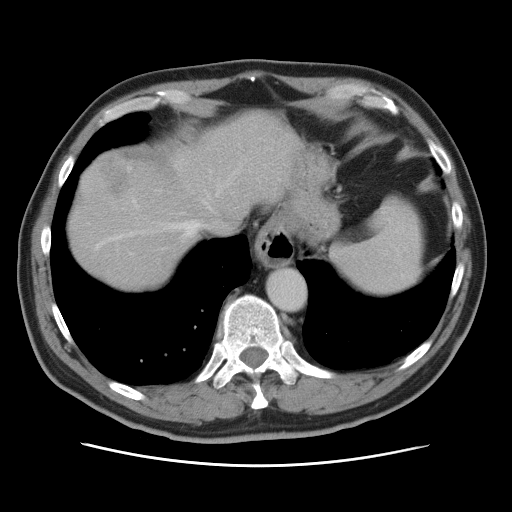
Contrast-enhanced abdominal CT, one axial slice. Slice 67 of 80 in the series (ordered by position). Intravenous contrast given. Soft-tissue window (W 400 / L 40 HU). 5 mm slice thickness. 512 × 512 image matrix, field of view 370 × 370 mm. Male patient, age 69 years. From the clinical record (not read from this slice): diagnosis: colorectal cancer liver metastases, imaged before liver resection; multiple liver metastases: no; largest metastasis: 5 cm; disease in both lobes: yes.
Structures marked on this image (outlined manually by an expert reader):
- hepatic veins: bounding box (x1, y1, x2, y2) in pixels: (97, 164, 242, 247)
- liver: (69, 111, 292, 290)
- planned liver remnant (the part of the liver to remain after resection): (69, 111, 292, 291)
- liver metastasis: (95, 156, 136, 198)